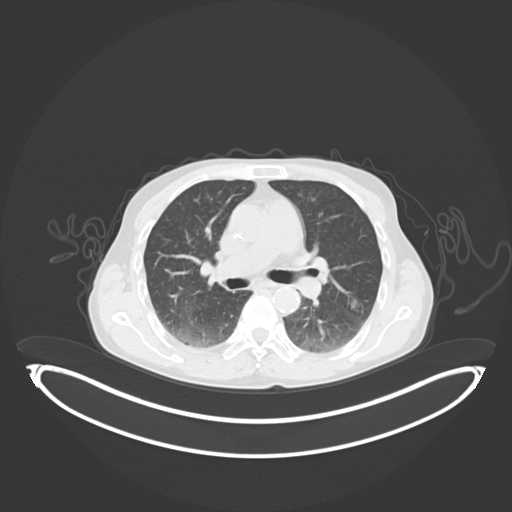
Chest CT, one axial slice; slice 59 of 102 in the series (ordered by position); lung window (W 1500 / L -600 HU); 3 mm slice thickness; 512 × 512 image matrix. Patient: male, 58 years. Case-level facts recorded for this patient, not image findings: clinical TNM (as recorded): T1c N0 M0; histopathological grade: G2.
Outlined on this slice (rectangle marked by the reading radiologist):
- lung tumour (recorded histology: adenocarcinoma): bounding box (x1, y1, x2, y2) in pixels: (348, 294, 365, 314)